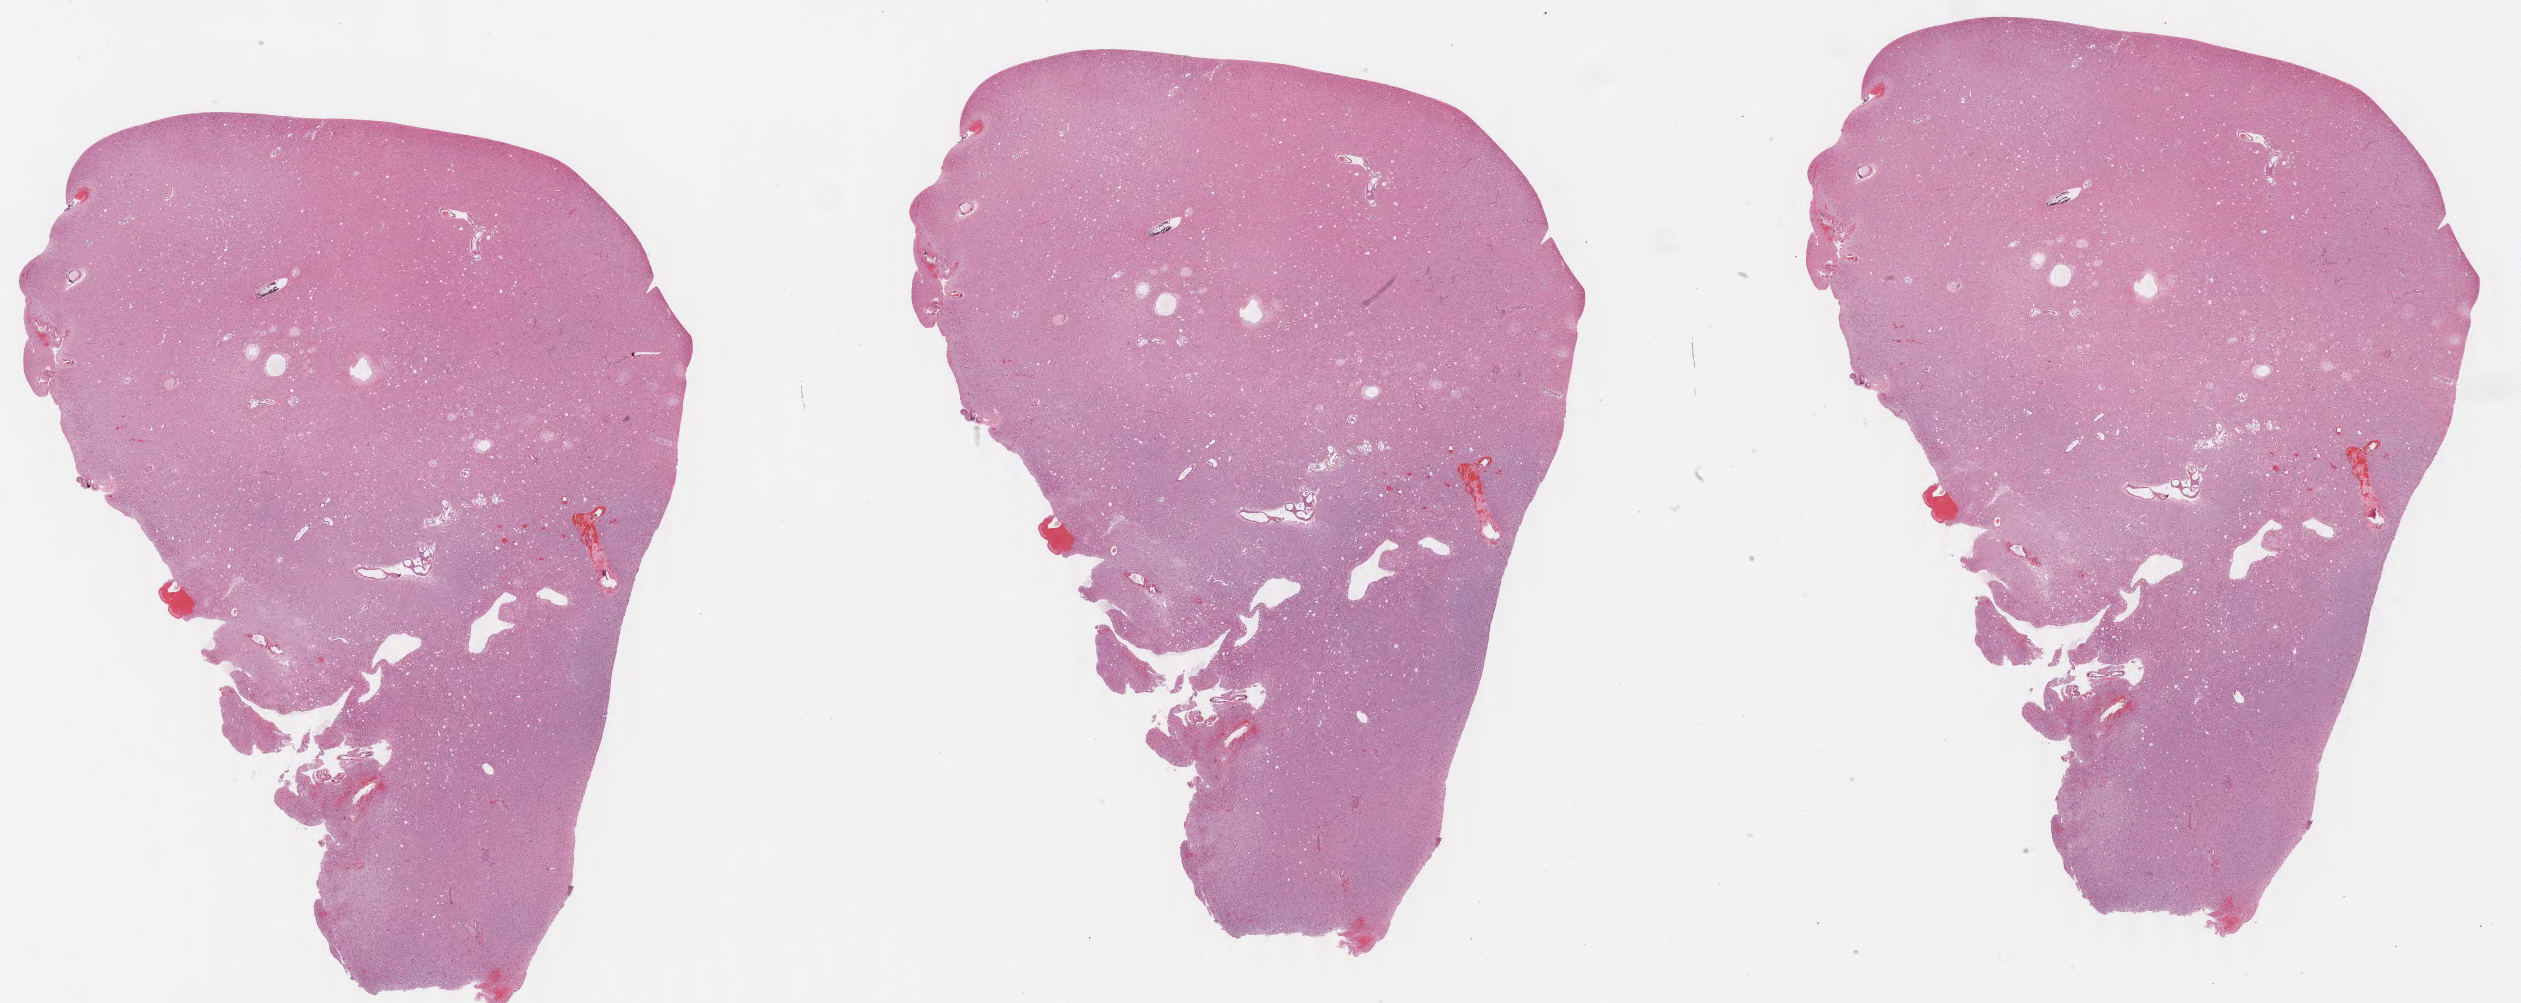
Whole-slide histology image, H&E — a low-resolution overview of the entire scanned area, about 39.9 x 15.9 mm (from a 40x scan). Formalin-fixed paraffin-embedded (FFPE) diagnostic section. Primary tumour sample from the brain. Male, age 54 years at initial diagnosis. Histologic grade: G2 (moderately differentiated).
Laterality: left. Histologic diagnosis: Oligodendroglioma, NOS (cerebrum).